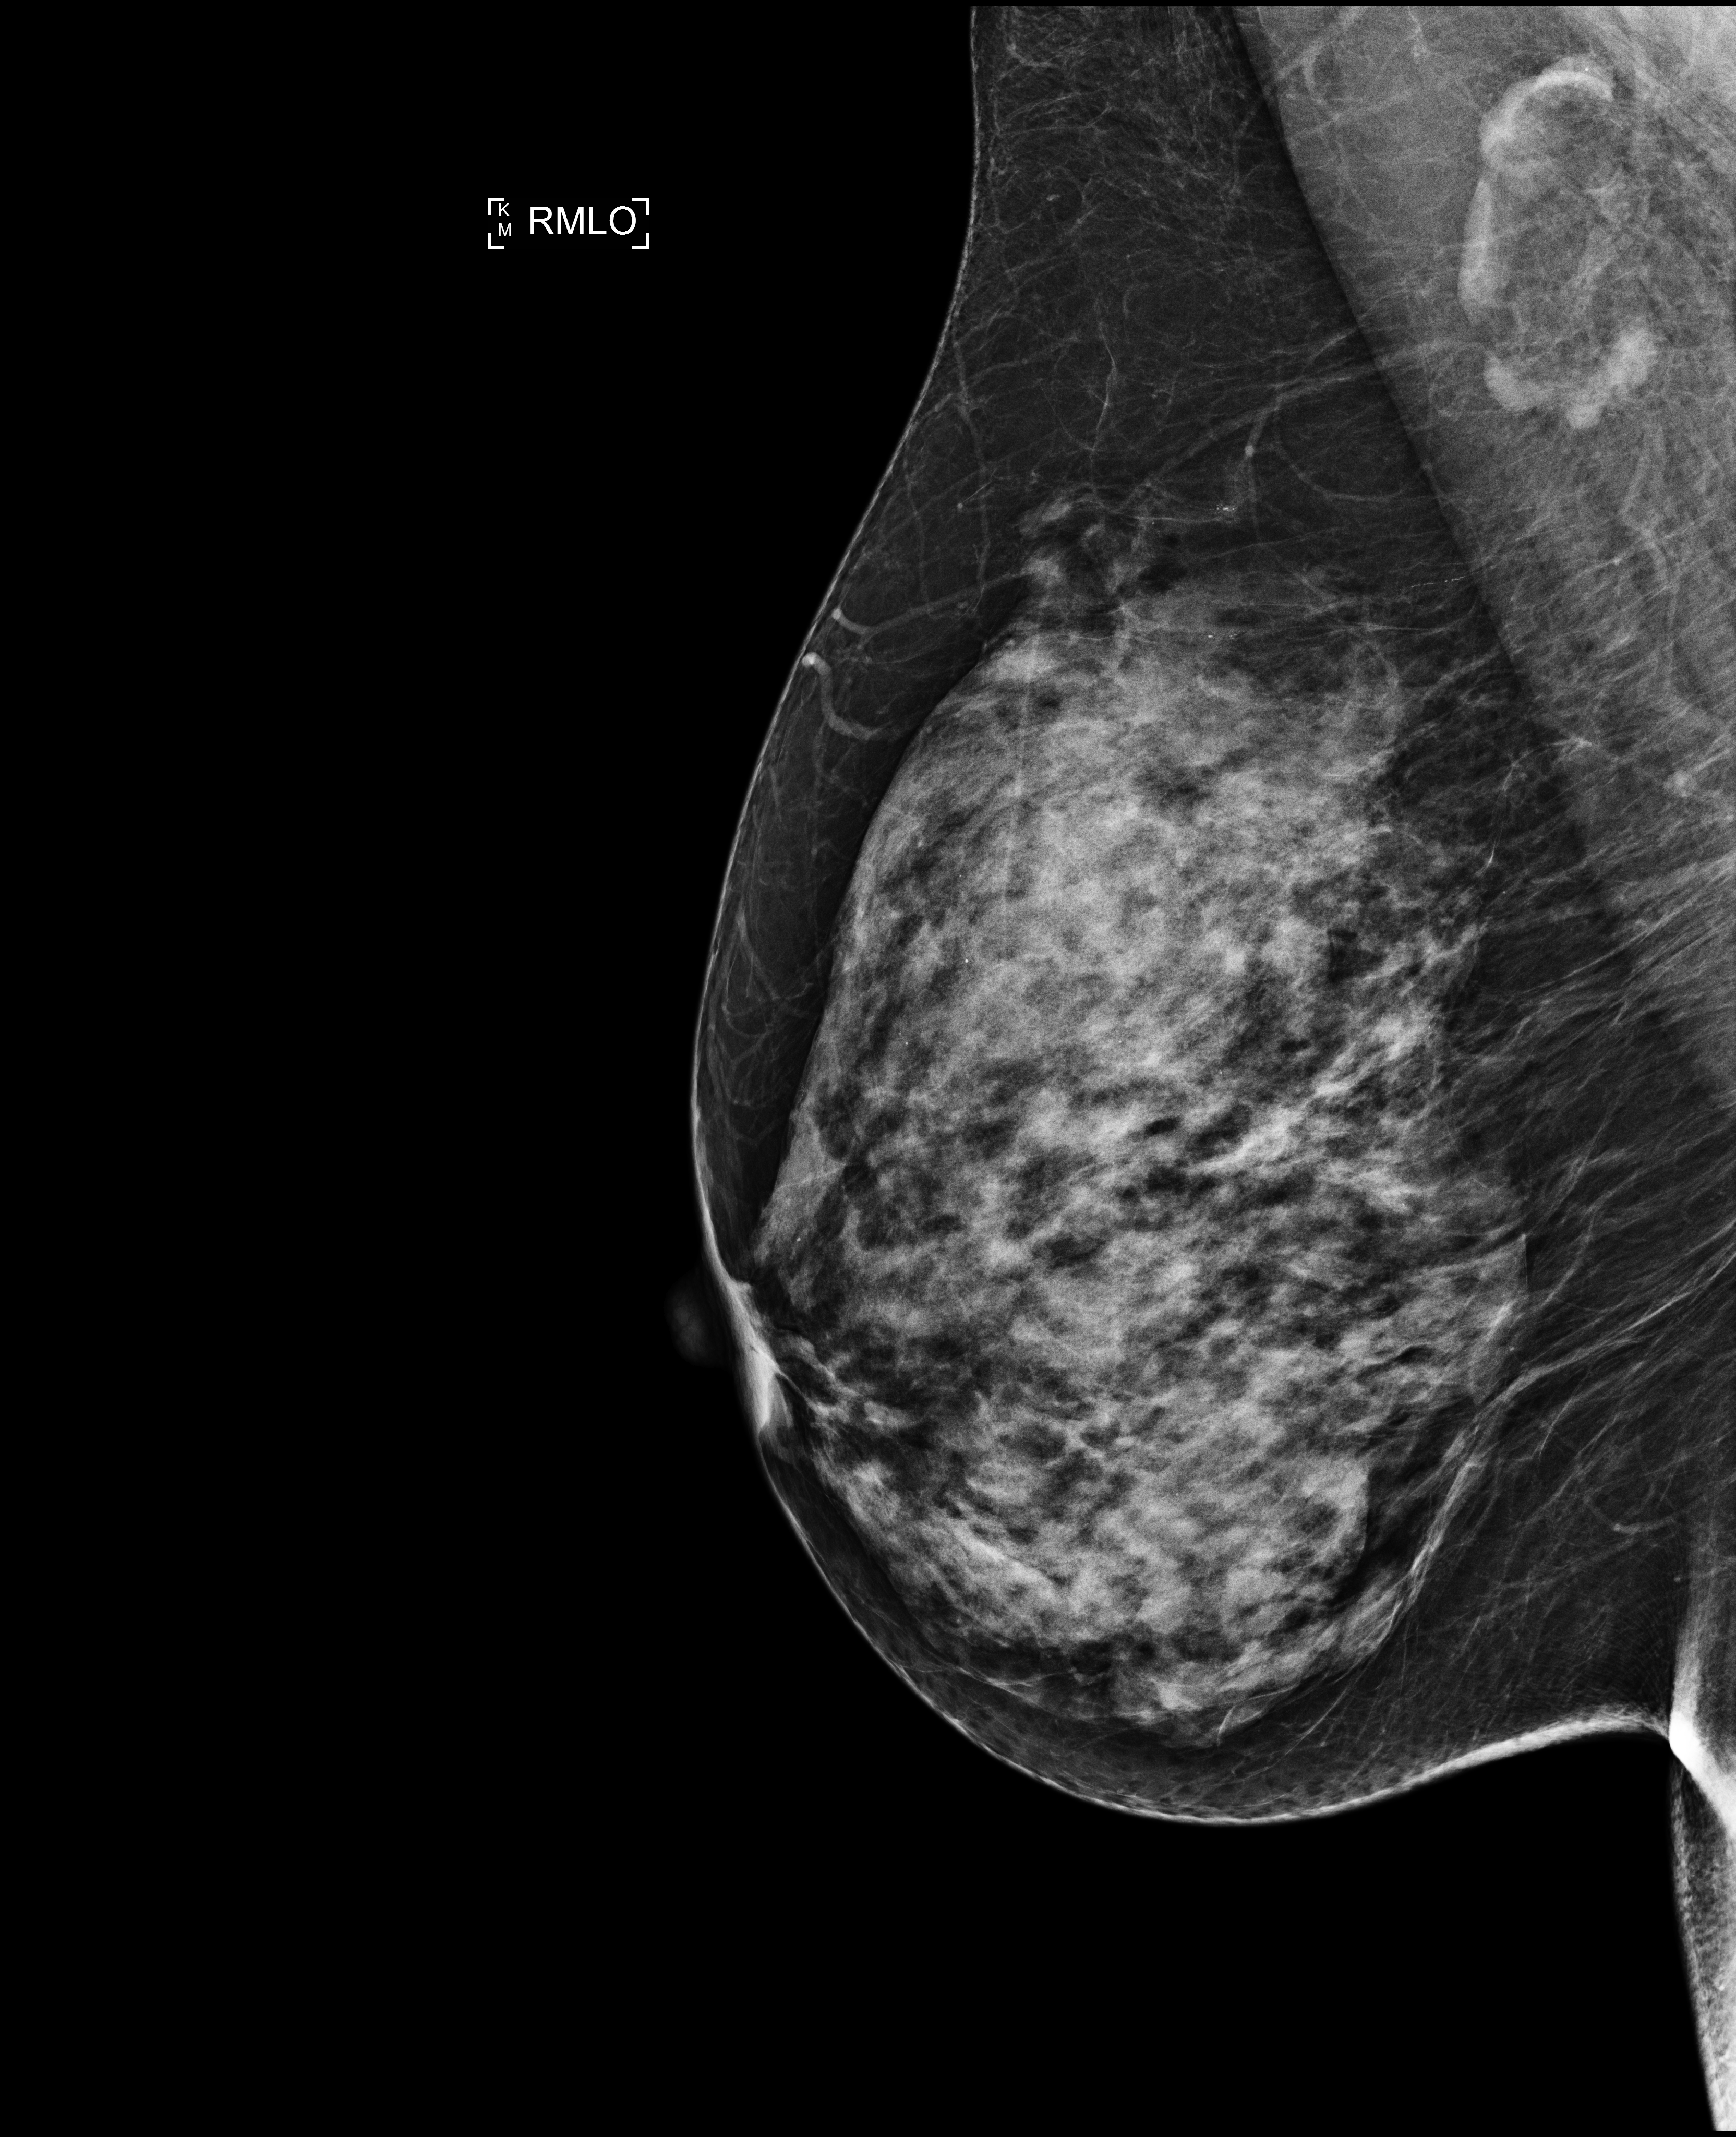
Full-field digital mammogram (FFDM), right breast, MLO view, annual screening mammography examination, compressed breast thickness 58 mm. Patient: female, 56 years.
Final BI-RADS category for the screening round (tomosynthesis exam, both breasts): category 2.